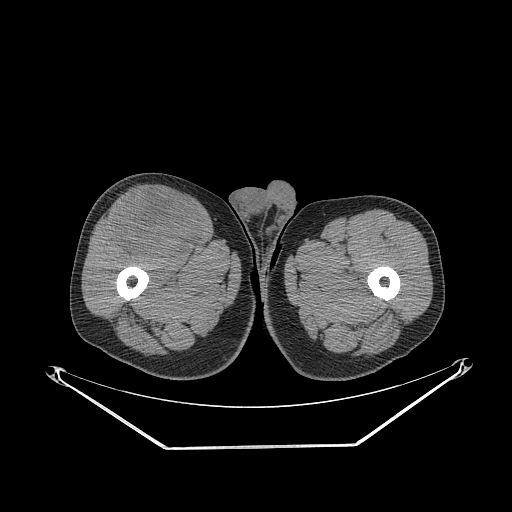
CT of an extremity soft-tissue mass (from a PET/CT study), one axial slice; reconstruction kernel STANDARD; 140 kVp; soft-tissue window (W 400 / L 40 HU); 3.75 mm slice thickness; 512 × 512 image matrix, field of view 500 × 500 mm. Male patient. Case-level facts recorded for this patient, not image findings: histological type: pleiomorphic leiomyosarcoma; grade: intermediate; site of the primary tumour: right thigh.
Outlined on this slice (expert contour drawn on MRI and transferred to this co-registered scan by the dataset authors):
- gross tumour volume including surrounding oedema: bounding box (x1, y1, x2, y2) in pixels: (112, 192, 202, 259)
- gross tumour volume (mass): (112, 192, 202, 259)